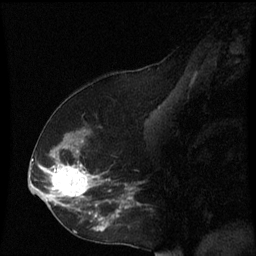
Breast MRI (dynamic contrast-enhanced), one sagittal slice; dynamic contrast-enhanced series, image 2 of 3 at this slice position (ordered by acquisition); 1.5 T; TE 4.2 ms, TR 8.9 ms; 256 × 256 image matrix, field of view 200 × 200 mm. Patient: female, 53 years. From the clinical record (not read from this slice): setting: breast cancer imaged before/during neoadjuvant chemotherapy; receptor status: HR-positive, HER2-negative.
Outlined on this slice (semi-automatic segmentation, software-assisted and operator-edited):
- analysis volume of interest (the breast-tissue region the enhancement analysis was run in; not a lesion): box from (x=38, y=128) to (x=139, y=231) px
- tumour enhancement mask (voxels above the 70 % enhancement threshold inside the analysis volume of interest): (x=44, y=150)–(x=123, y=231)